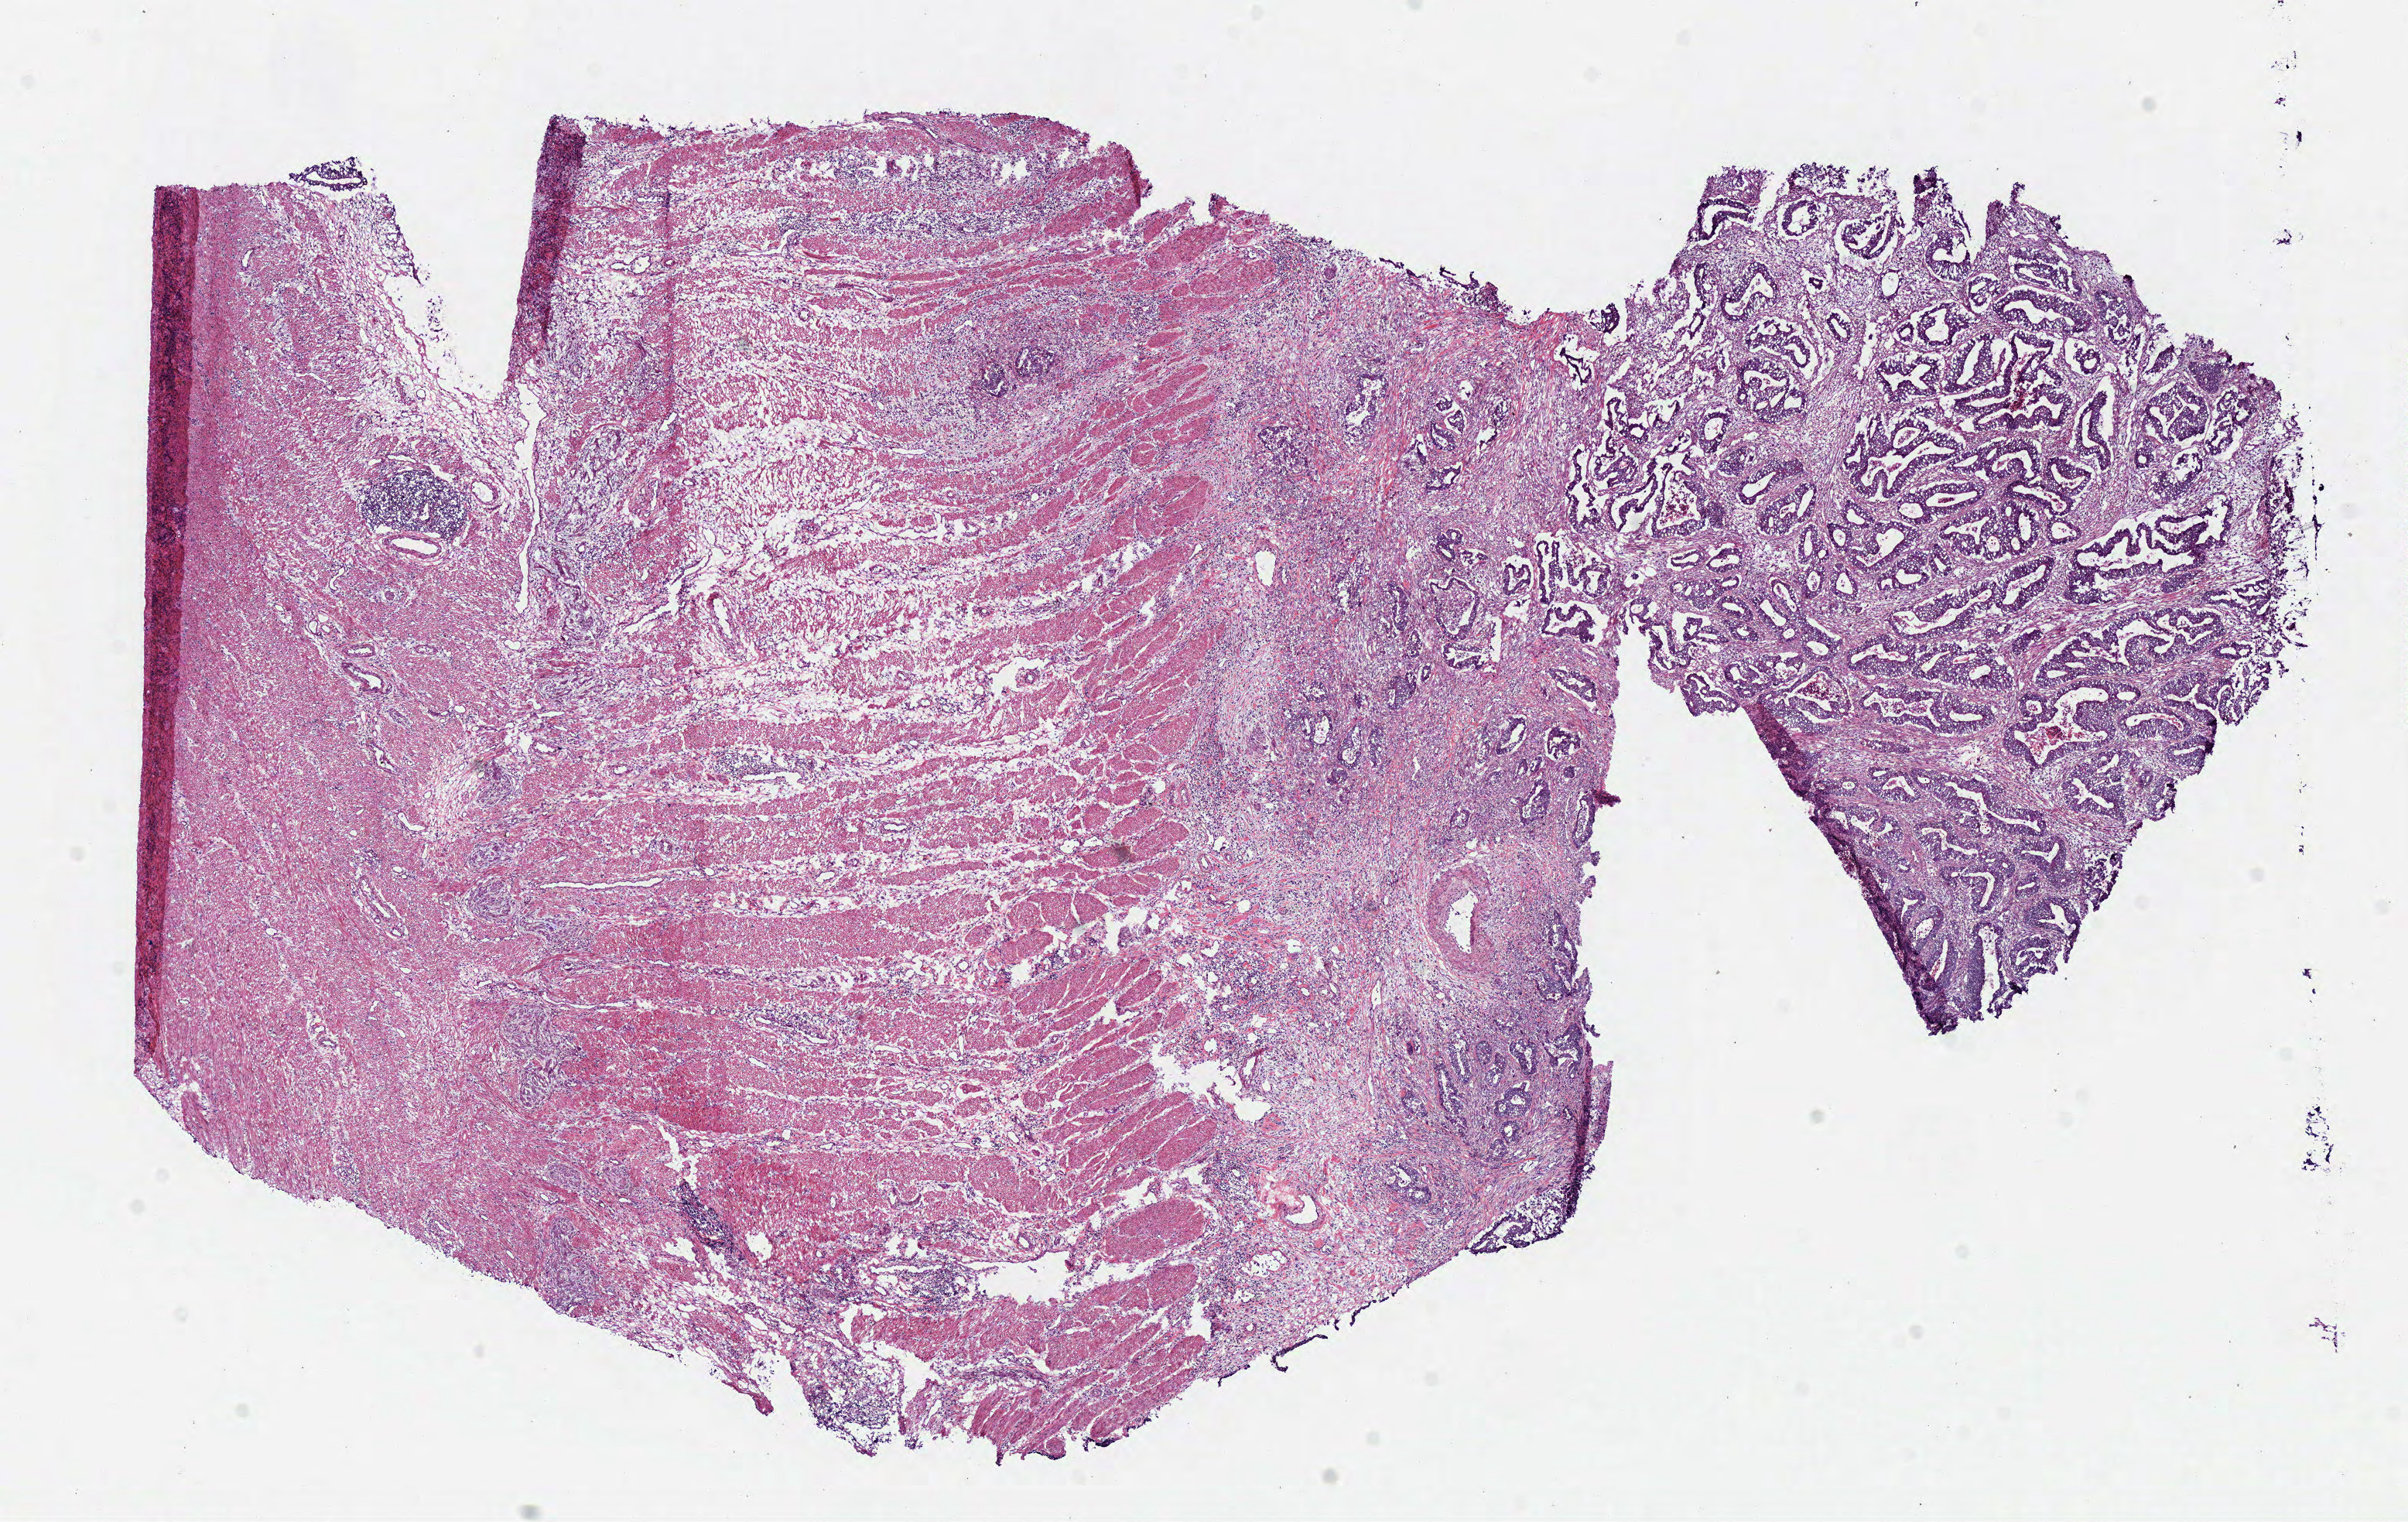
Digitized Hematoxylin and eosin (H&E) stained tissue section (whole slide) — whole scanned area (about 12.2 x 7.7 mm, slide scanned at 40x) shown as a low-resolution overview. Frozen section from the bottom of the tissue portion. Sample: primary tumour, colon. Female patient; age at initial diagnosis 76 years. Pathologist review of this section (percent, as recorded): tumour cells 35%, tumour nuclei 50%, normal cells 0%, stromal cells 60%, necrosis 5%.
• AJCC pathologic stage: IV
• histologic diagnosis: Adenocarcinoma, NOS (cecum)
• lymph nodes positive (case pathology): 50 of 59 examined